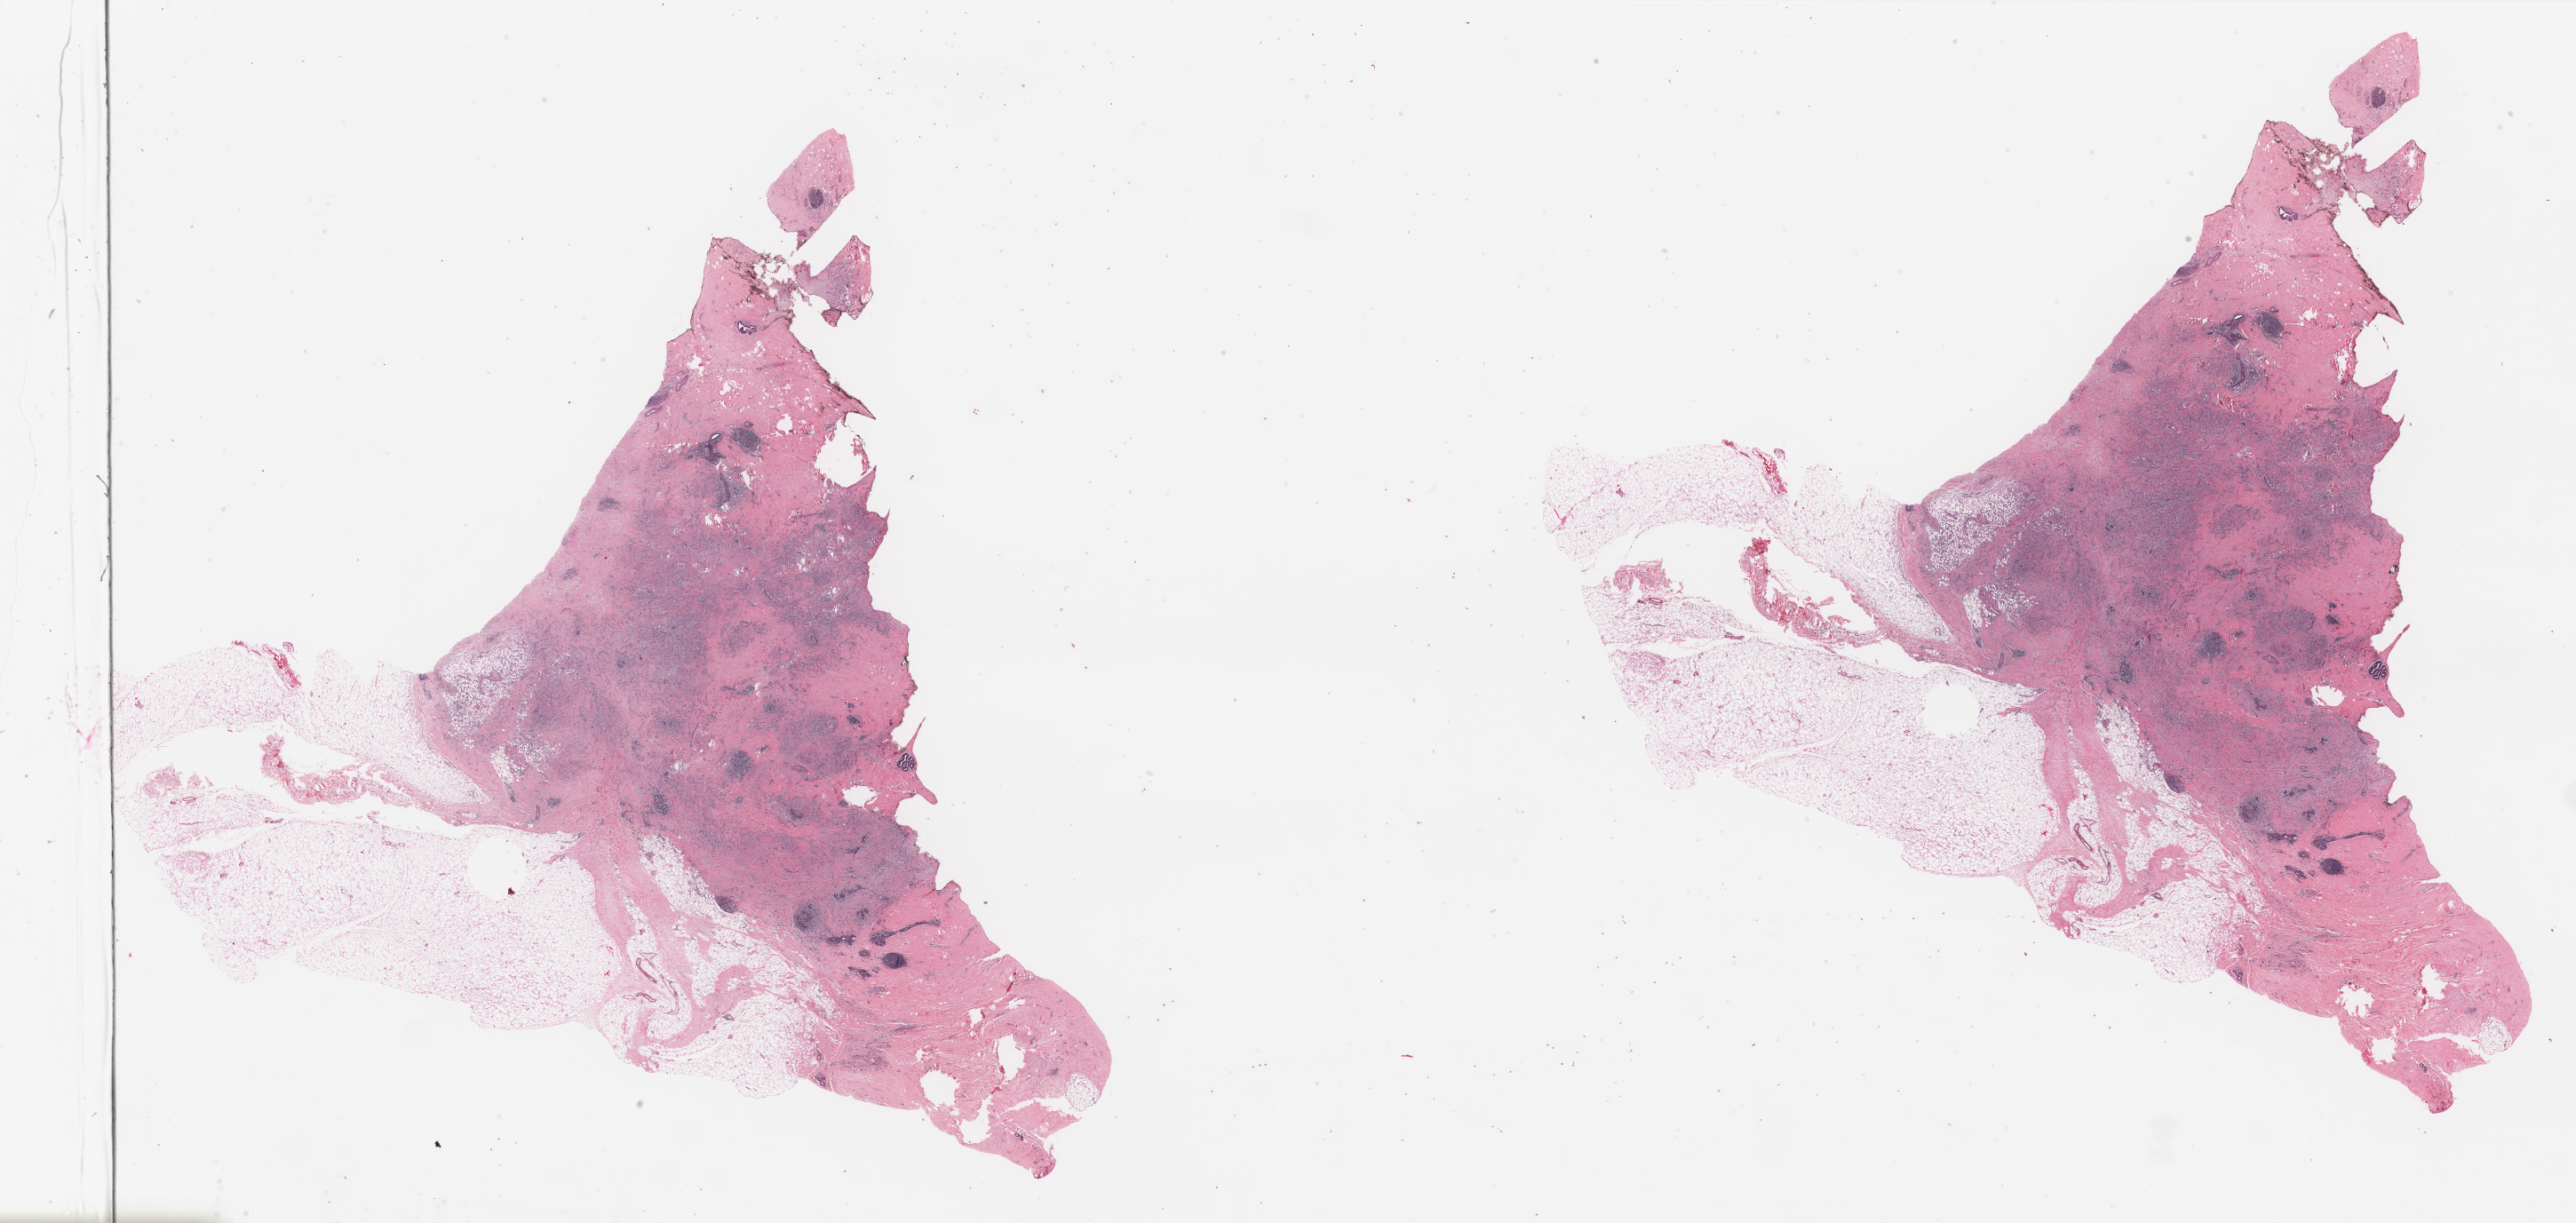
Digitized H&E-stained tissue section (whole slide), a low-resolution overview of the entire scanned area, about 45.9 x 21.8 mm (acquisition: 40x scan). Formalin-fixed paraffin-embedded (FFPE) diagnostic section. Breast, primary tumour sample. Female, age 55 years at initial diagnosis.
Histologic diagnosis: Lobular carcinoma, NOS.